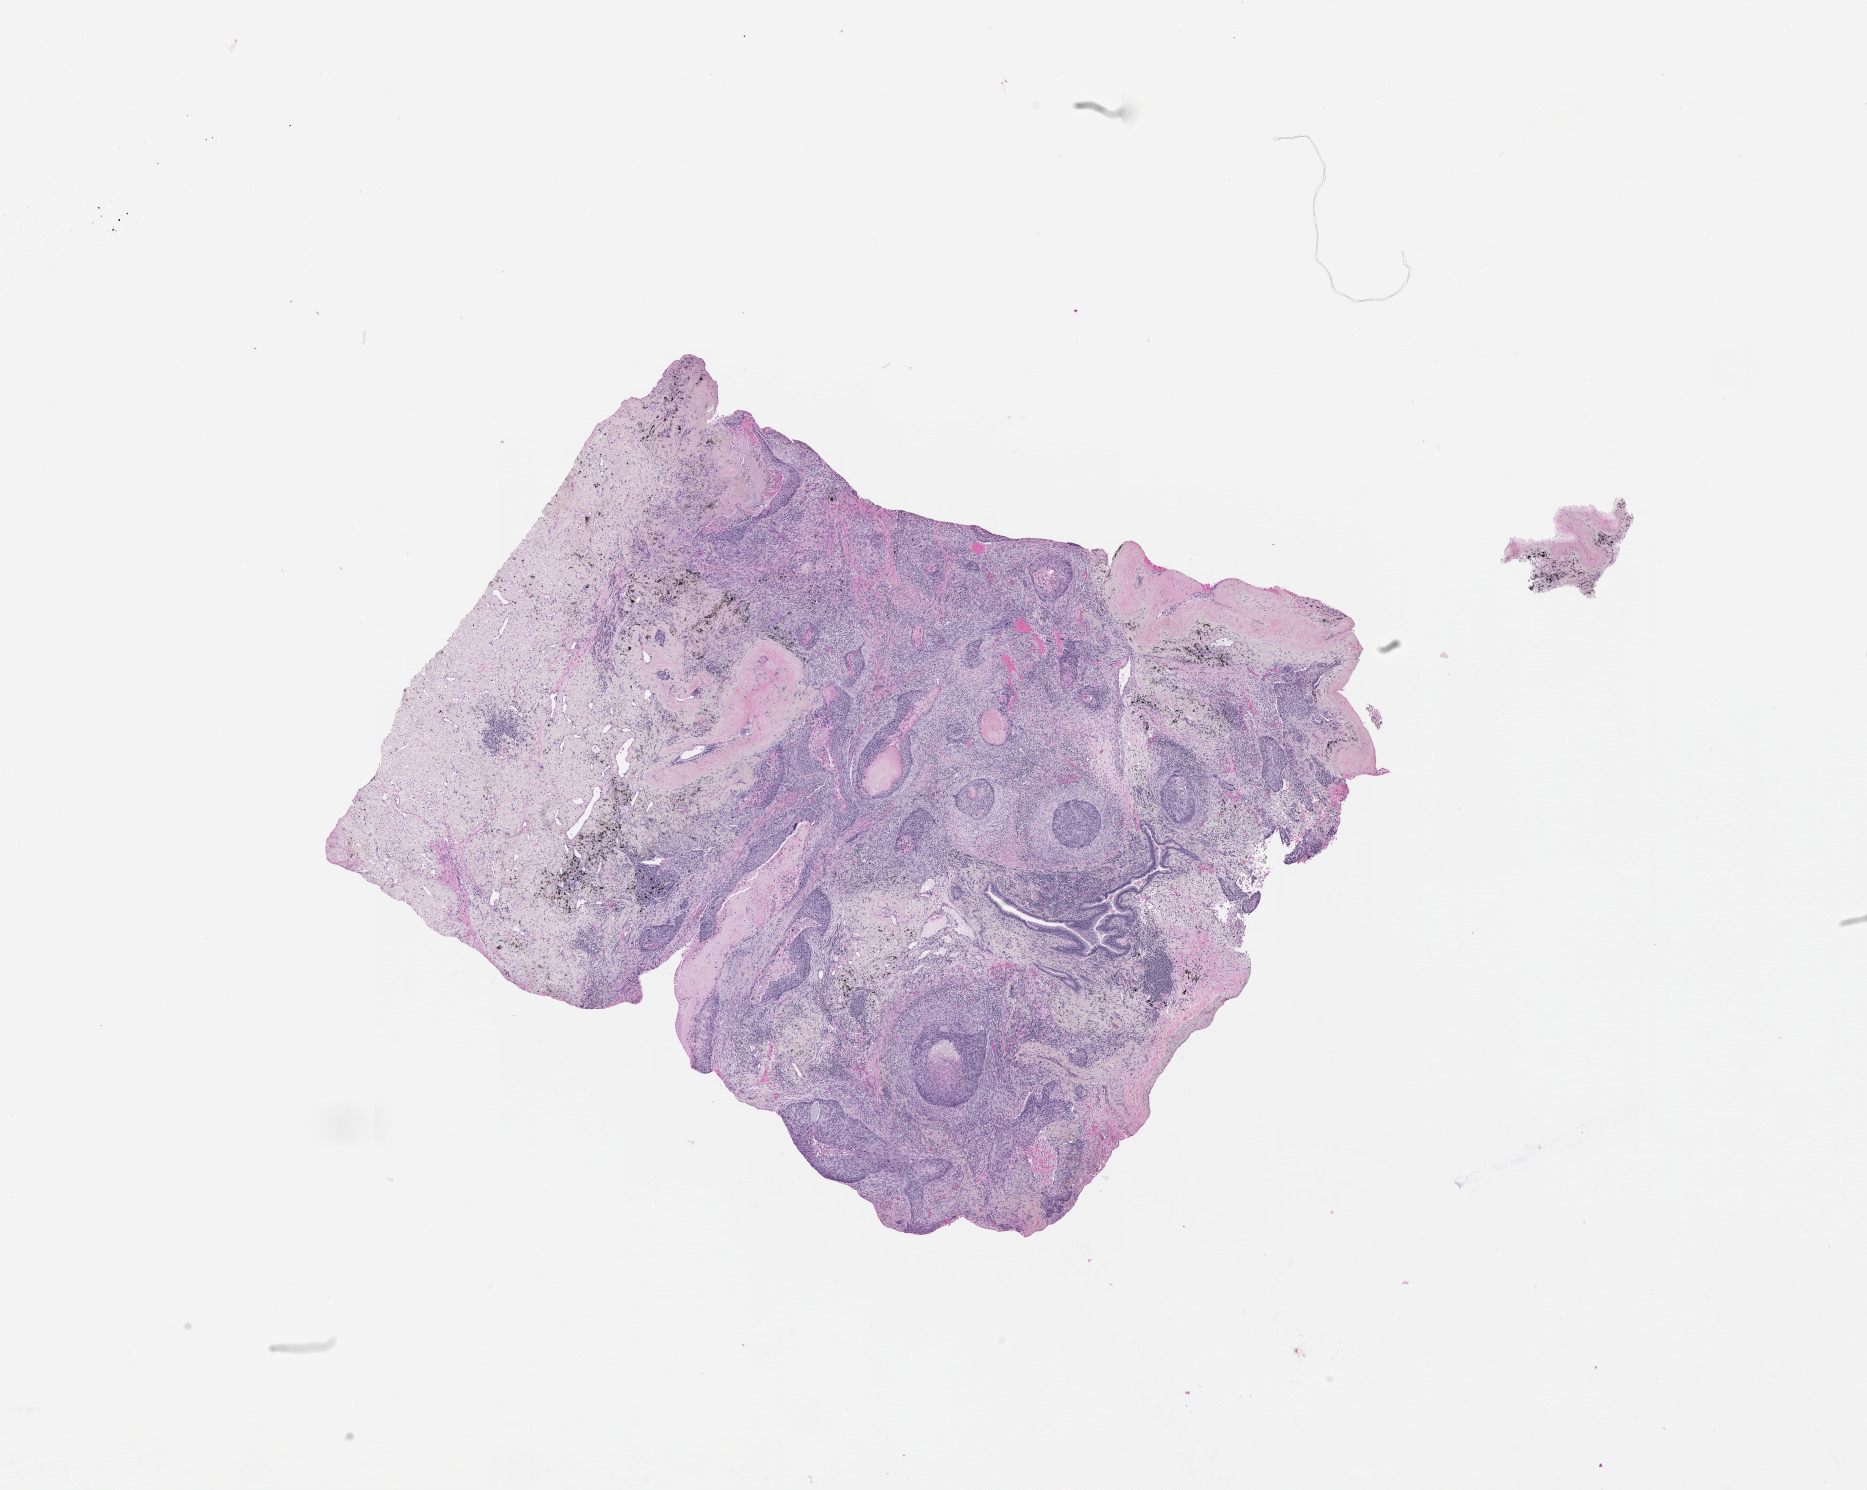
Digitized H&E tissue section (whole slide), whole scanned area (about 15.0 x 12.0 mm) shown as a low-resolution overview, lung, tumour tissue. Patient sex: female.
Patient diagnosis (cohort enrolment): squamous cell carcinoma (lung).